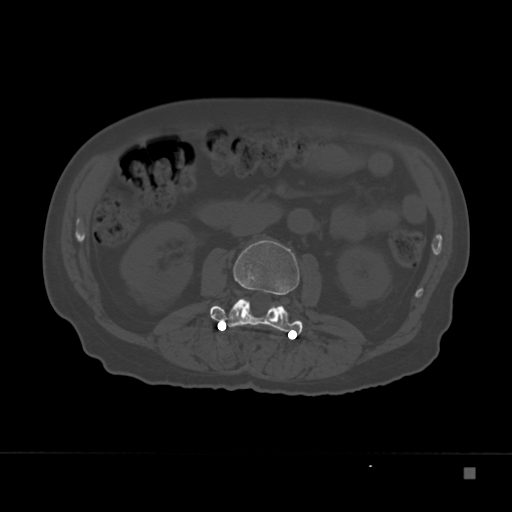
CT including the spine, one axial slice; position 84 of 332 along the scan axis; bone window (W 1800 / L 400 HU); 1.5 mm slice thickness; 512 × 512 image matrix, field of view 389 × 389 mm. Patient: male, 72 years. From the clinical record (not read from this slice): primary cancer: skeletal.
Structures marked on this image (semi-automatically segmented with operator editing):
- L2 vertebra: bounding box <211,240,303,335> (left, top, right, bottom; pixels)
- L3 vertebra: <211,297,299,332>